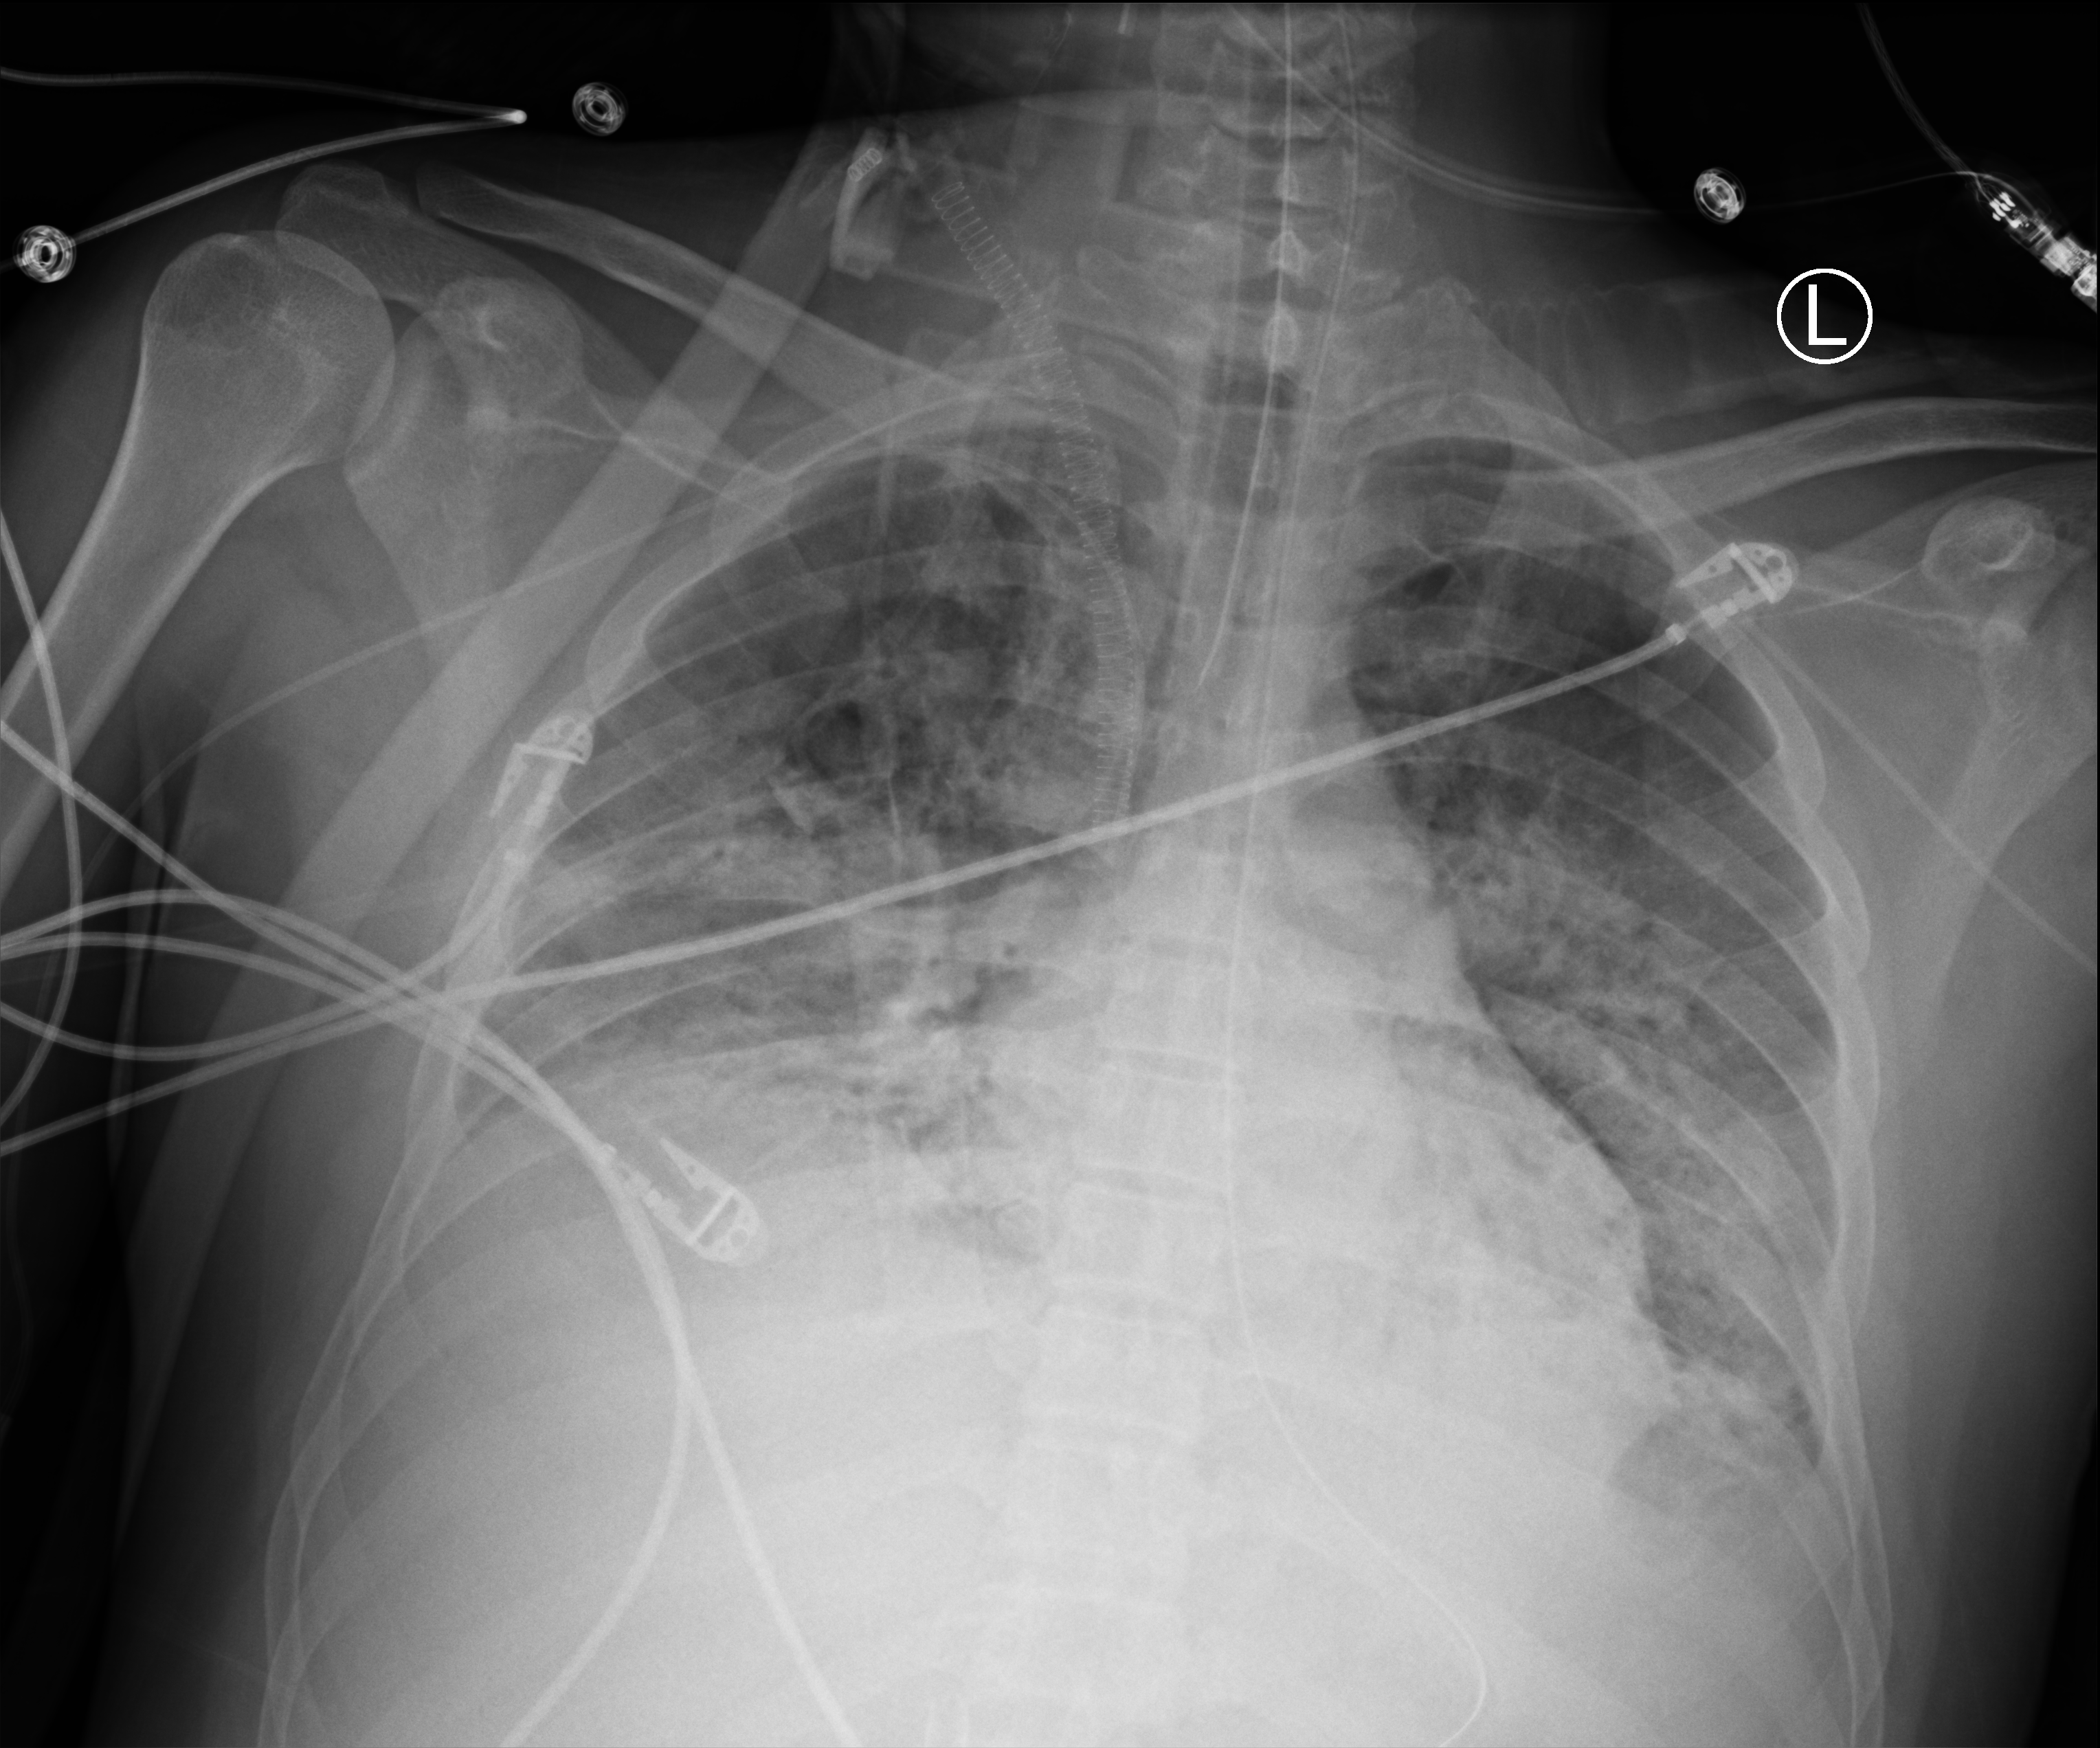
Chest X-ray (portable), anteroposterior (AP) projection. Adult patient hospitalised with COVID-19, age 18–59 years.
Hospital-stay facts (about this admission, not read from this image; timing relative to this image not recorded): COPD (admission record): no; mechanically ventilated during this hospital stay: yes; admitted to intensive care during this hospital stay: yes.